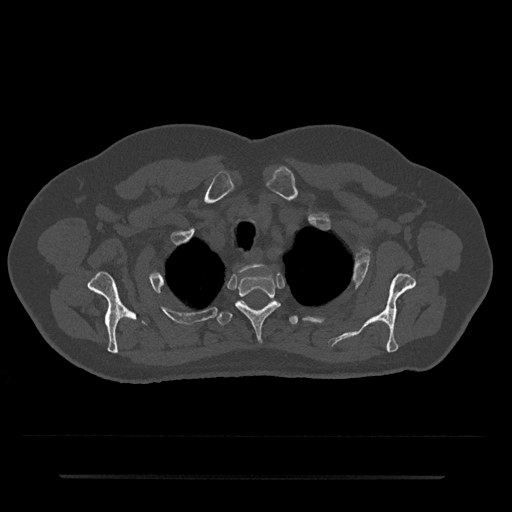
CT including the spine, one axial slice; slice 599 of 797 in the series (ordered by position); reconstruction kernel Br40s/3; 120 kVp; bone window (W 1800 / L 400 HU); 0.5 mm slice thickness; 512 × 512 image matrix. Patient: male, 69 years. Case-level facts recorded for this patient, not image findings: primary cancer: prostate.
Outlined on this slice (semi-automatically segmented with operator editing):
- T1 vertebra: bounding box <241,264,259,272> (left, top, right, bottom; pixels)
- T2 vertebra: <235,273,280,339>
- T3 vertebra: <217,301,298,325>